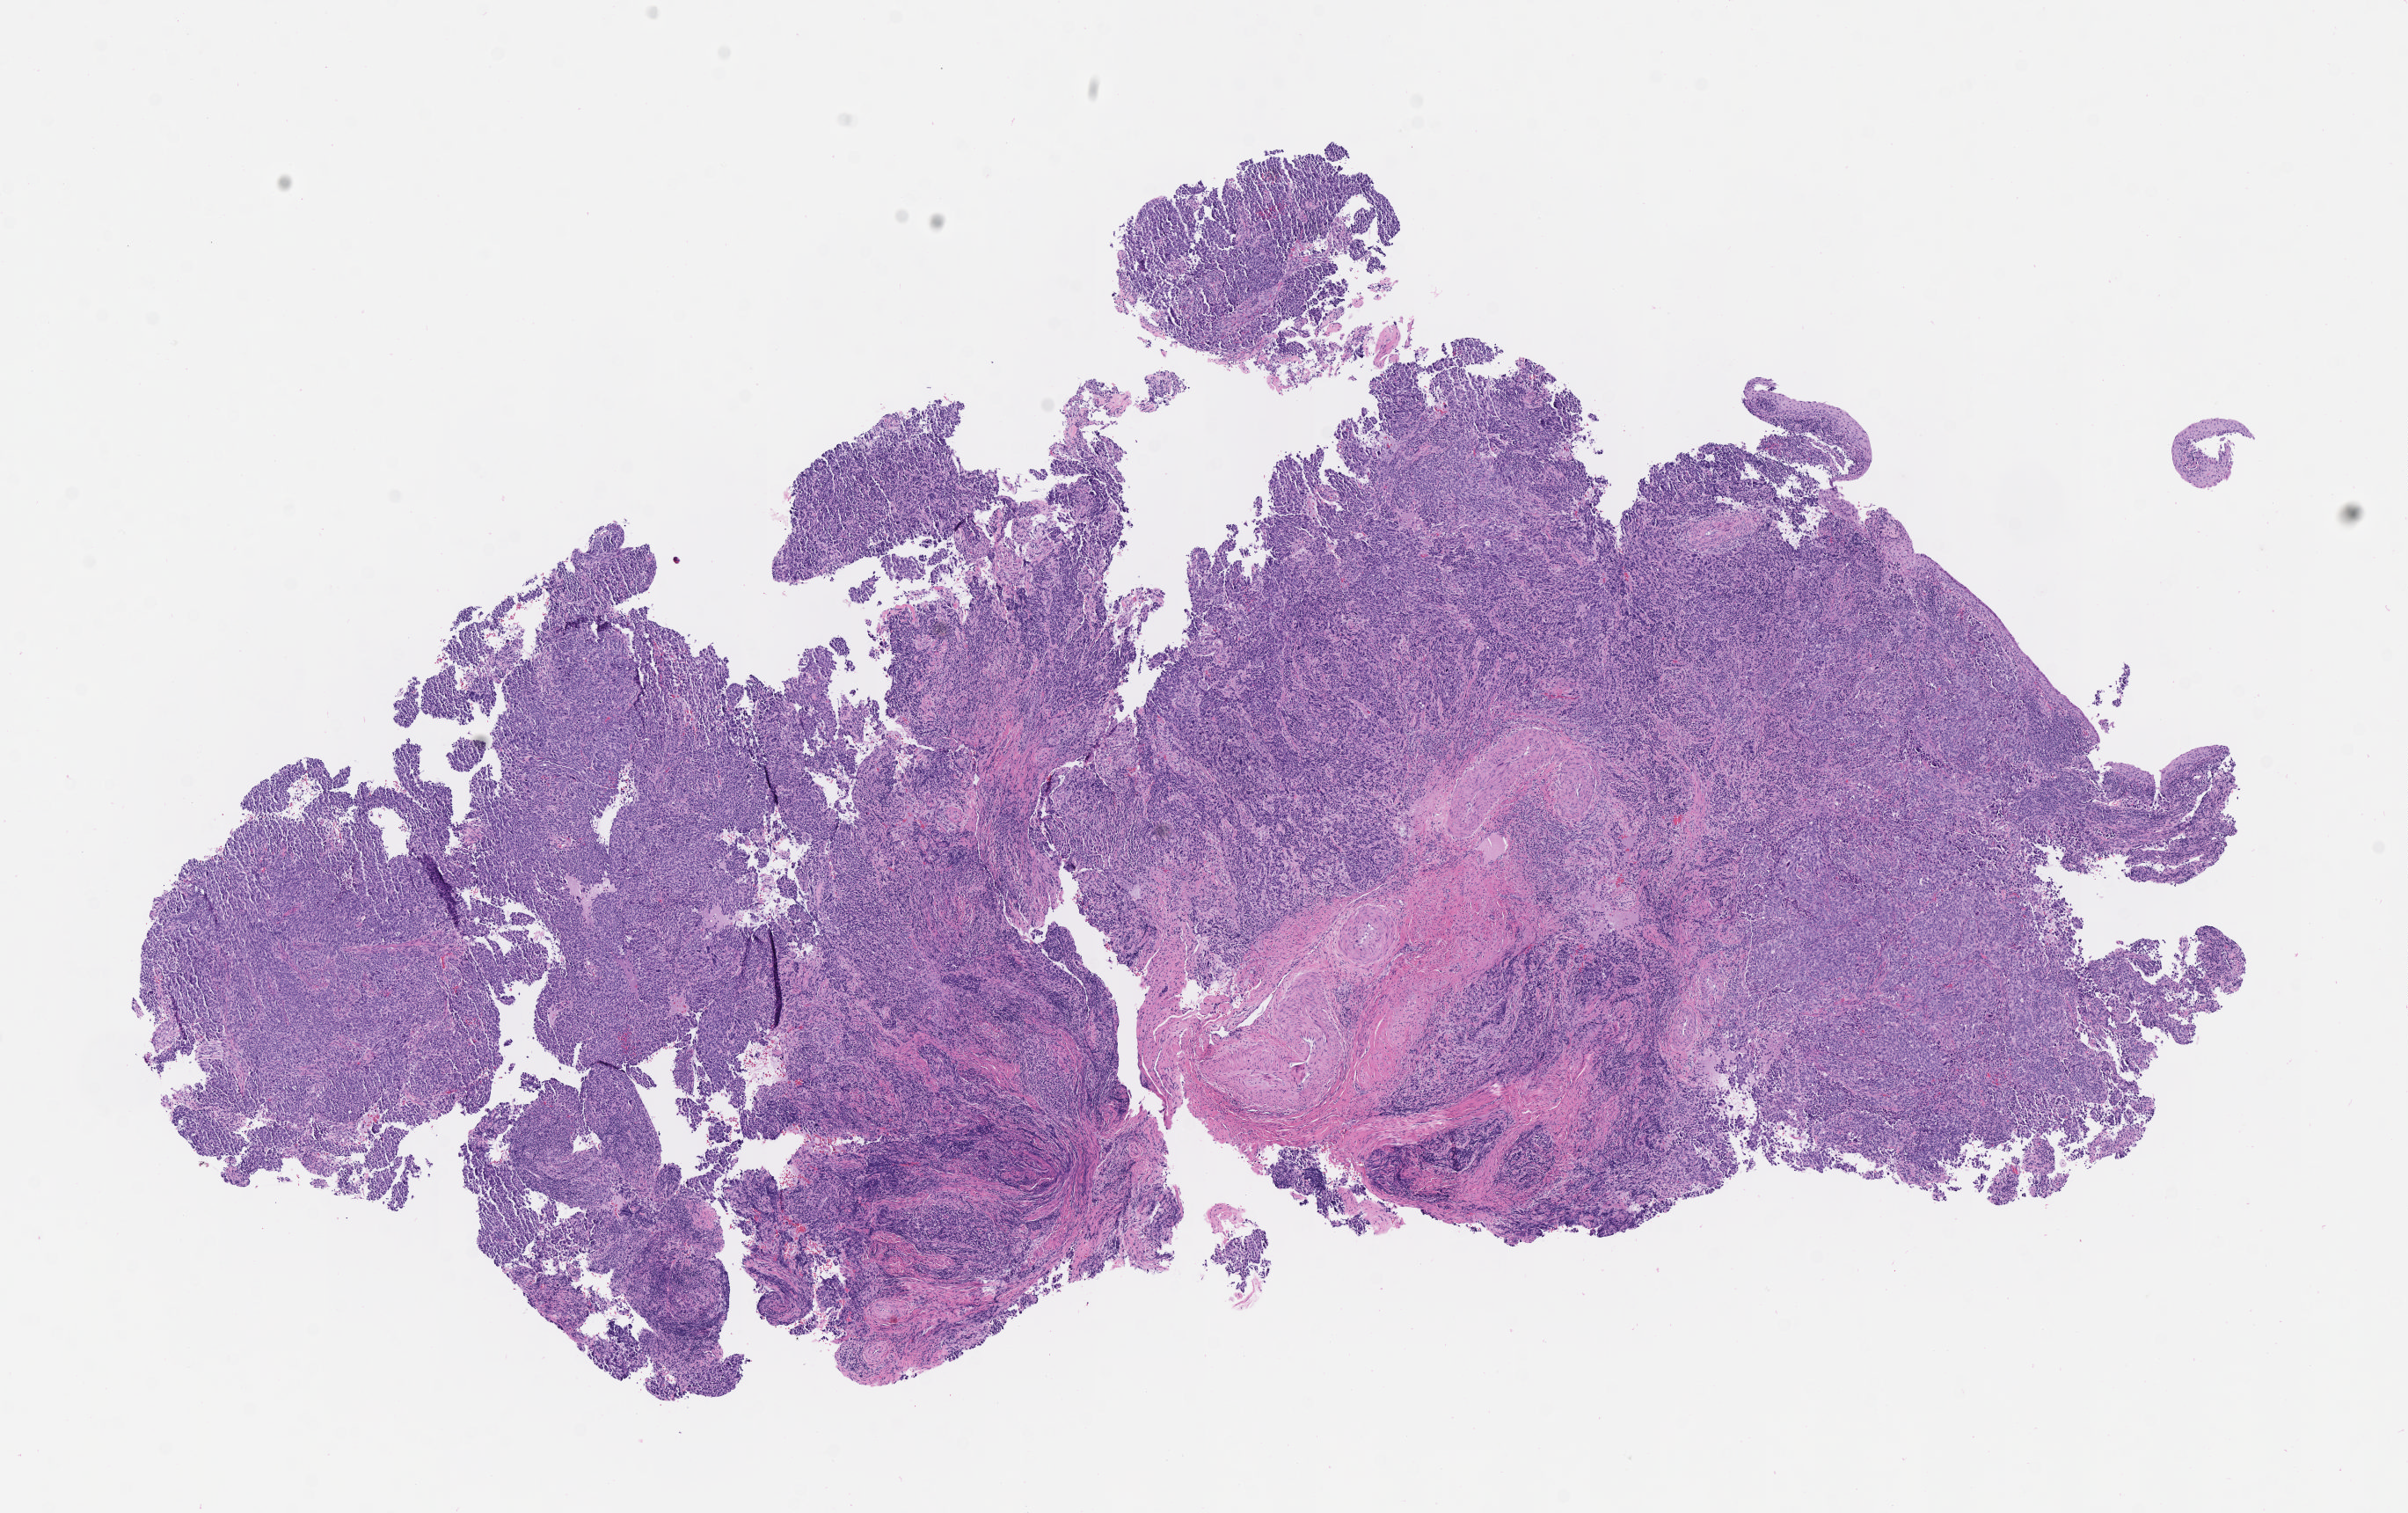
Digitized haematoxylin and eosin-stained section — shown as a low-resolution overview of the whole scanned area (about 11.1 x 7.0 mm), specimen: tumor tissue, site: cervix. Patient: female, age 48 years.
Diagnosis: Squamous cell carcinoma, large cell, nonkeratinizing, NOS.